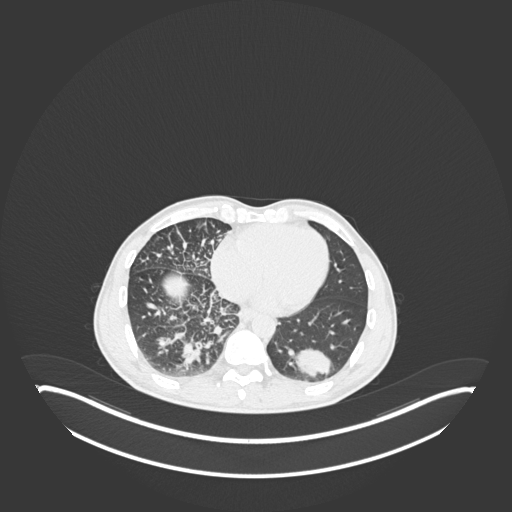
Chest CT, one axial slice; position 73 of 237 along the scan axis; reconstruction kernel B30f; 120 kVp; lung window (W 1500 / L -600 HU); 1 mm slice thickness; 512 × 512 image matrix, field of view 500 × 500 mm. Patient: male, 49 years. Case-level facts recorded for this patient, not image findings: clinical TNM (as recorded): T2b N1 M0.
Structures marked on this image (rectangle marked by the reading radiologist):
- lung tumour (recorded histology: adenocarcinoma): box from (x=294, y=345) to (x=335, y=380) px